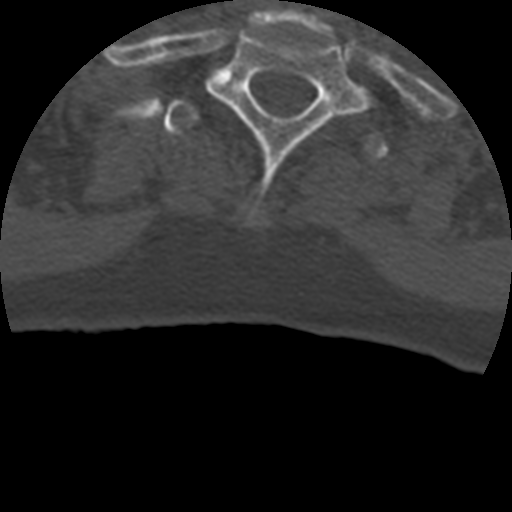
CT including the spine, one axial slice; position 383 of 399 along the scan axis; 120 kVp; bone window (W 1800 / L 400 HU); 1.25 mm slice thickness; 512 × 512 image matrix, field of view 160 × 160 mm. Patient age 69 years. Case-level facts recorded for this patient, not image findings: primary cancer: prostate.
Outlined on this slice (semi-automatically segmented with operator editing):
- T1 vertebra: bounding box [x1, y1, x2, y2] px = [207, 24, 369, 217]
- T2 vertebra: [163, 97, 389, 161]